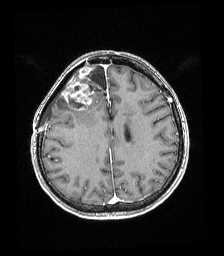
Brain MRI from a brain-tumour surgery series, one axial slice. Position 68 of 192 along the scan axis. T1-weighted post-contrast. 224 × 256 image matrix, field of view 219 × 250 mm. From the clinical record (not read from this slice): histopathology: Astrocytoma; WHO grade: 4; IDH mutation: yes; tumour location: Right superficial frontal.
Annotated regions visible in this slice (expert manual segmentation):
- tumour: bounding box (x1, y1, x2, y2) in pixels: (63, 64, 92, 111)